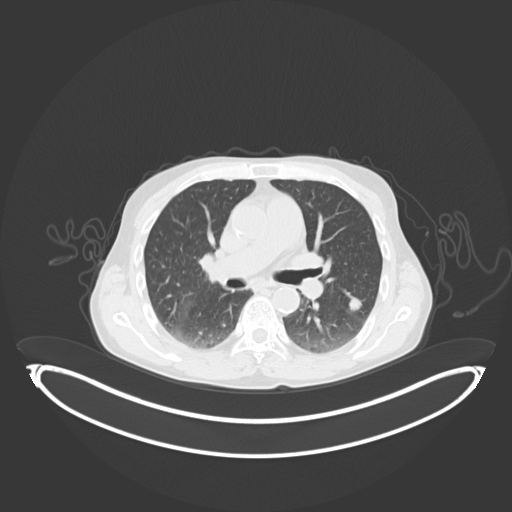
Chest CT, one axial slice; slice 57 of 102 in the series (ordered by position); reconstruction kernel B30f; 120 kVp; lung window (W 1500 / L -600 HU); 3 mm slice thickness; 512 × 512 image matrix, field of view 500 × 500 mm. Male patient, age 58 years. Case-level facts recorded for this patient, not image findings: clinical TNM (as recorded): T1c N0 M0; histopathological grade: G2.
Outlined on this slice (rectangle marked by the reading radiologist):
- lung tumour (recorded histology: adenocarcinoma): box from (x=344, y=289) to (x=365, y=315) px